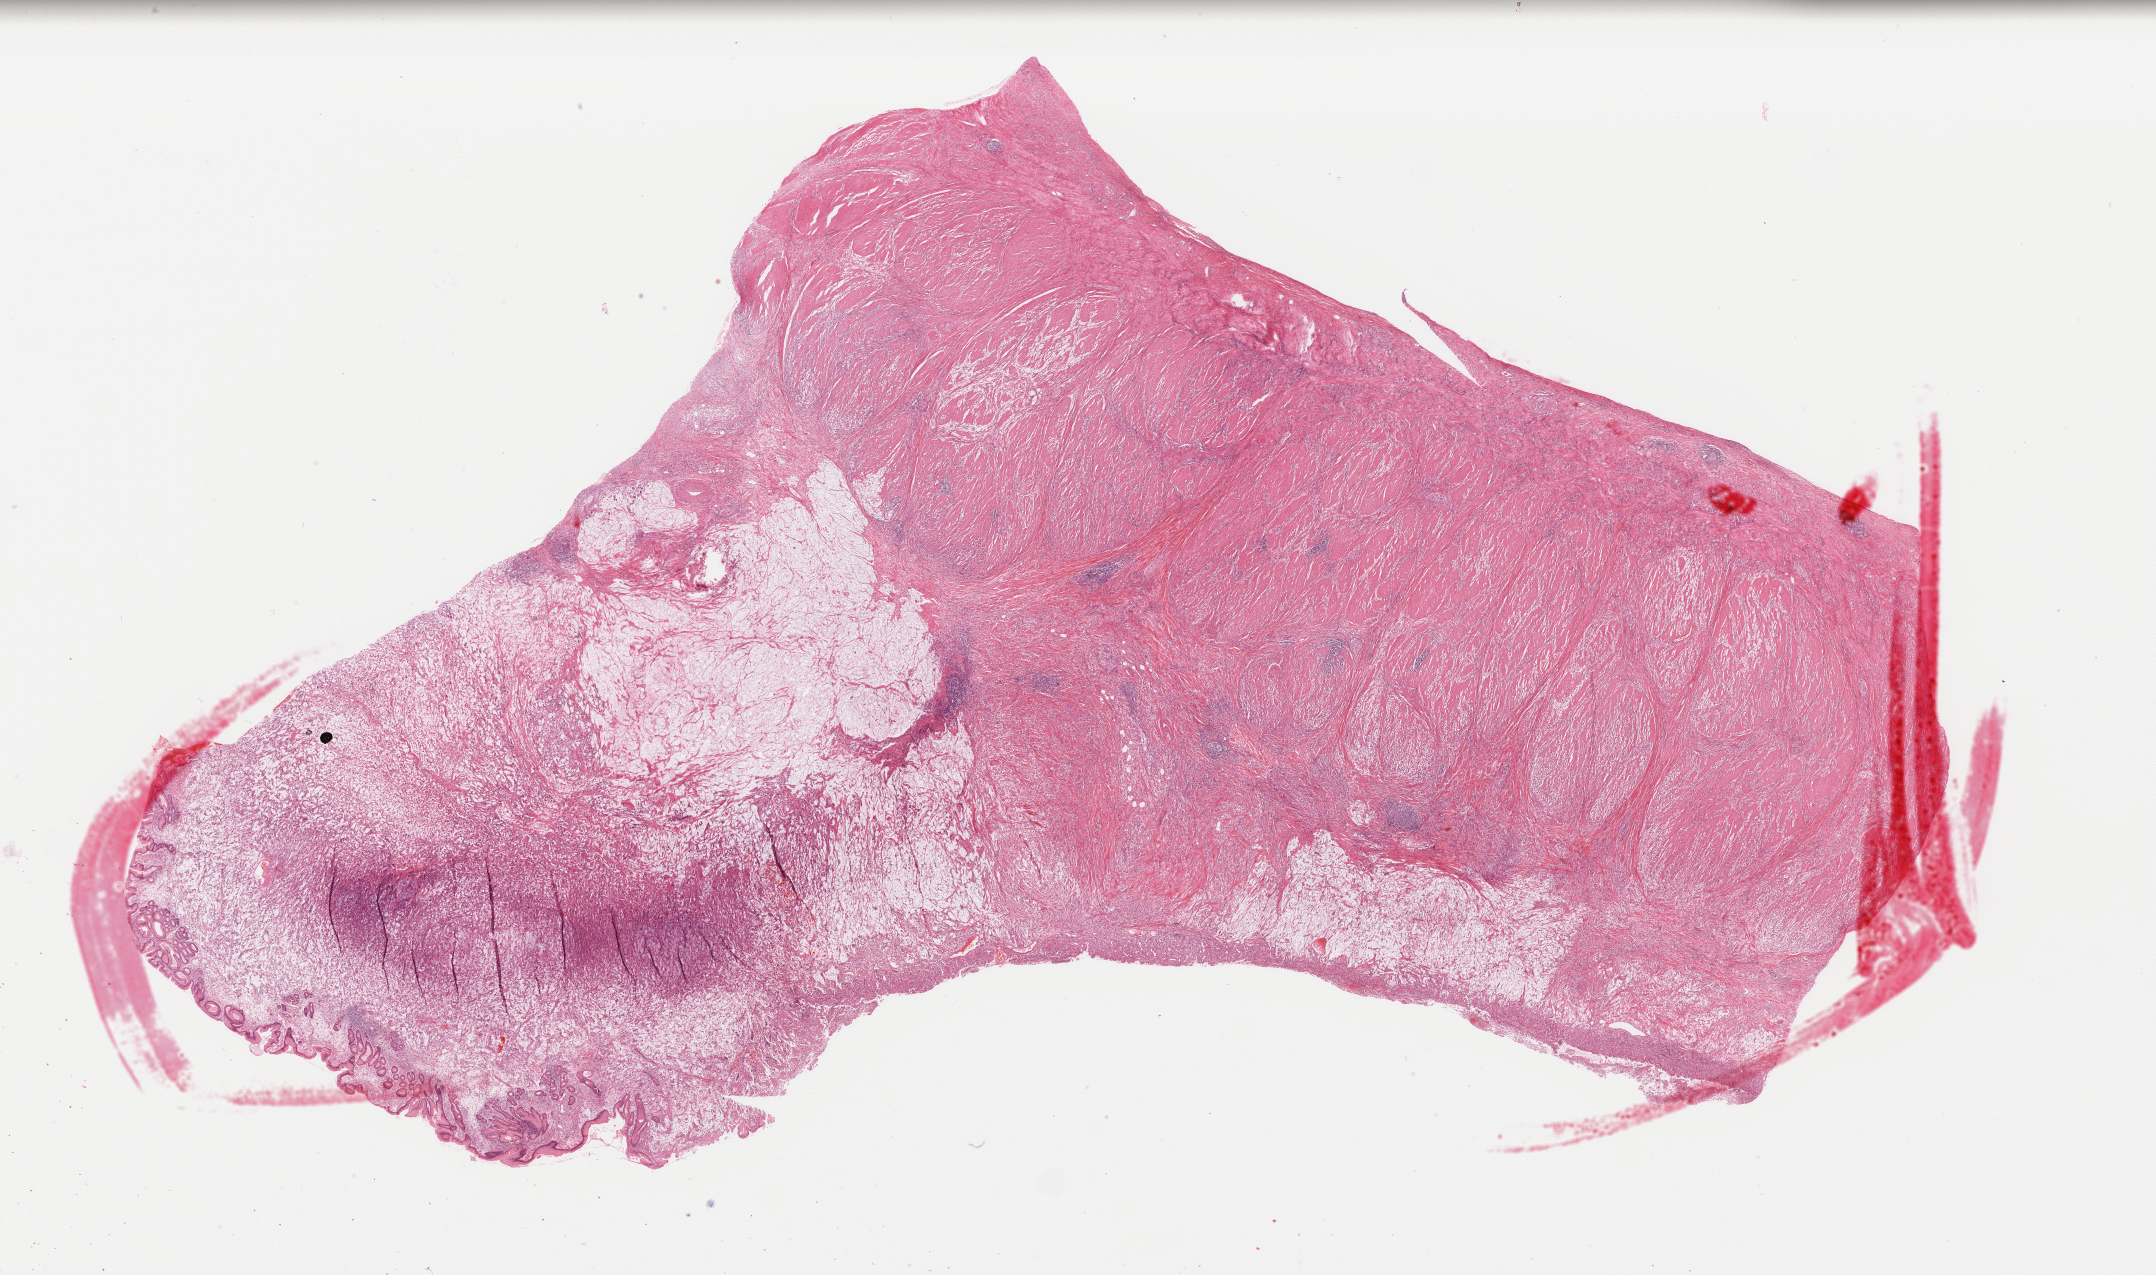
Hematoxylin and eosin (H&E) stained whole-slide image, shown as a low-resolution overview of the whole scanned area (about 34.1 x 20.1 mm). Formalin-fixed paraffin-embedded (FFPE) diagnostic section. Stomach, primary tumour sample. Male patient; age at initial diagnosis 55 years. Histologic grade: G3 (poorly differentiated).
Diagnosis: Adenocarcinoma, NOS (gastric antrum). AJCC pathologic stage: IIA (7th edition). Lymph nodes positive (case pathology): 0 of 10 examined.